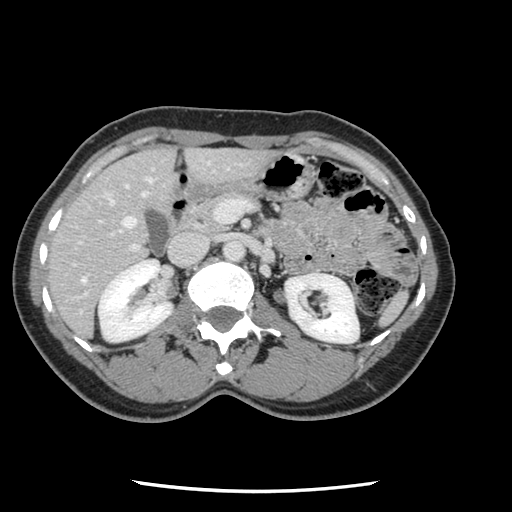
Contrast-enhanced abdominal CT, one axial slice. Position 53 of 134 along the scan axis. Intravenous contrast given. Soft-tissue window (W 400 / L 40 HU). 2.5 mm slice thickness. 512 × 512 image matrix. Female patient, age 43 years. Case-level facts recorded for this patient, not image findings: diagnosis: colorectal cancer liver metastases, imaged before liver resection; multiple liver metastases: yes.
Outlined on this slice (outlined manually by an expert reader):
- hepatic veins: bounding box (x1, y1, x2, y2) in pixels: (81, 177, 154, 284)
- liver: (49, 148, 269, 337)
- planned liver remnant (the part of the liver to remain after resection): (48, 148, 176, 331)
- portal vein (with intrahepatic branches): (72, 201, 252, 299)